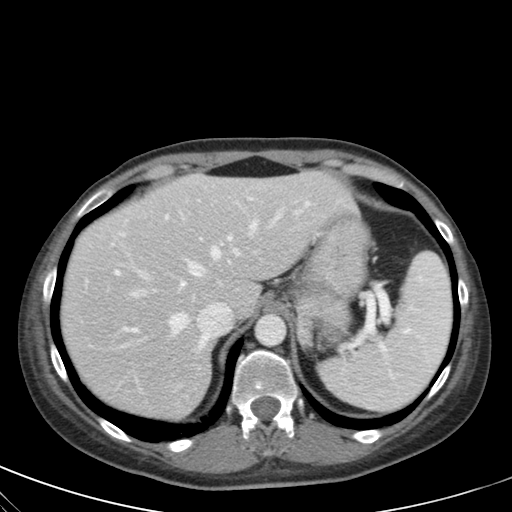
Contrast-enhanced abdominal CT, one axial slice. 120 kVp. Intravenous contrast given. Soft-tissue window (W 400 / L 40 HU). 4 mm slice thickness. 512 × 512 image matrix, field of view 350 × 350 mm. Female patient, age 28 years. From the clinical record (not read from this slice): diagnosis: adrenocortical carcinoma; tumour side: left adrenal; tumour size at pathology: 7 cm; Ki-67 index: 40 %; stage (as recorded): 4.
Outlined on this slice (semi-automatically segmented with operator editing):
- mass: bounding box [x1, y1, x2, y2] px = [296, 291, 349, 350]